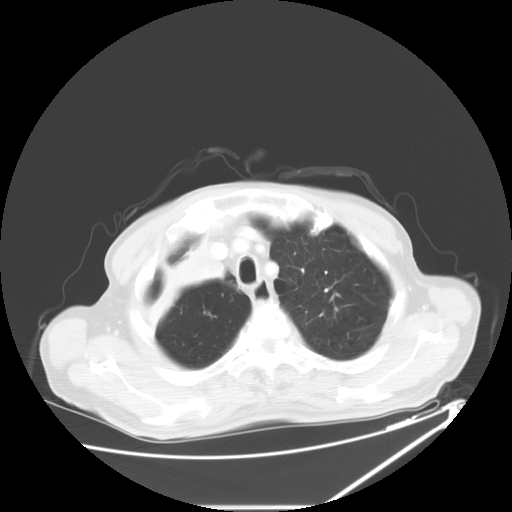
Chest CT, one axial slice; position 51 of 60 along the scan axis; lung window (W 1500 / L -600 HU); 5 mm slice thickness; 512 × 512 image matrix, field of view 410 × 410 mm. Patient: male, 73 years. From the clinical record (not read from this slice): clinical TNM (as recorded): T2a N1 M0.
Annotated regions visible in this slice (bounding box drawn by a radiologist):
- lung tumour (recorded histology: squamous cell carcinoma): bounding box (x1, y1, x2, y2) in pixels: (134, 233, 218, 339)